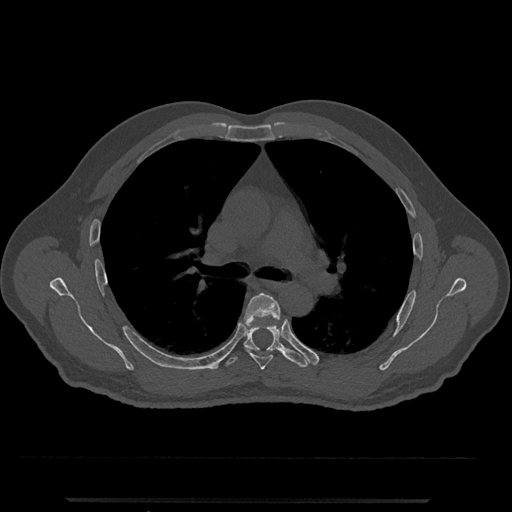
CT including the spine, one axial slice. Reconstruction kernel Br40s/3. 120 kVp. Bone window (W 1800 / L 400 HU). 0.5 mm slice thickness. 512 × 512 image matrix. Male patient, age 63 years. From the clinical record (not read from this slice): primary cancer: prostate.
Outlined on this slice (semi-automatically segmented with operator editing):
- T5 vertebra: bounding box [x1, y1, x2, y2] px = [244, 292, 281, 370]
- T6 vertebra: [224, 319, 309, 368]